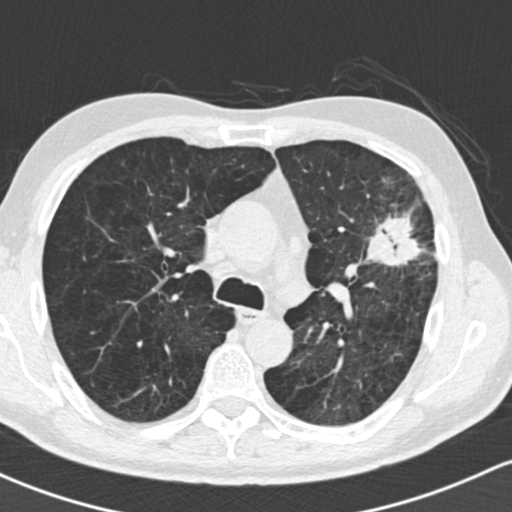
Low-dose screening chest CT, one axial slice; slice 102 of 162 in the series (ordered by position); 120 kVp; lung window (W 1500 / L -600 HU); 512 × 512 image matrix, field of view 318 × 318 mm.
Structures marked on this image (outlined manually by an expert reader):
- lesion 1 (tumor, upper lobe of left lung): box from (x=363, y=212) to (x=427, y=267) px